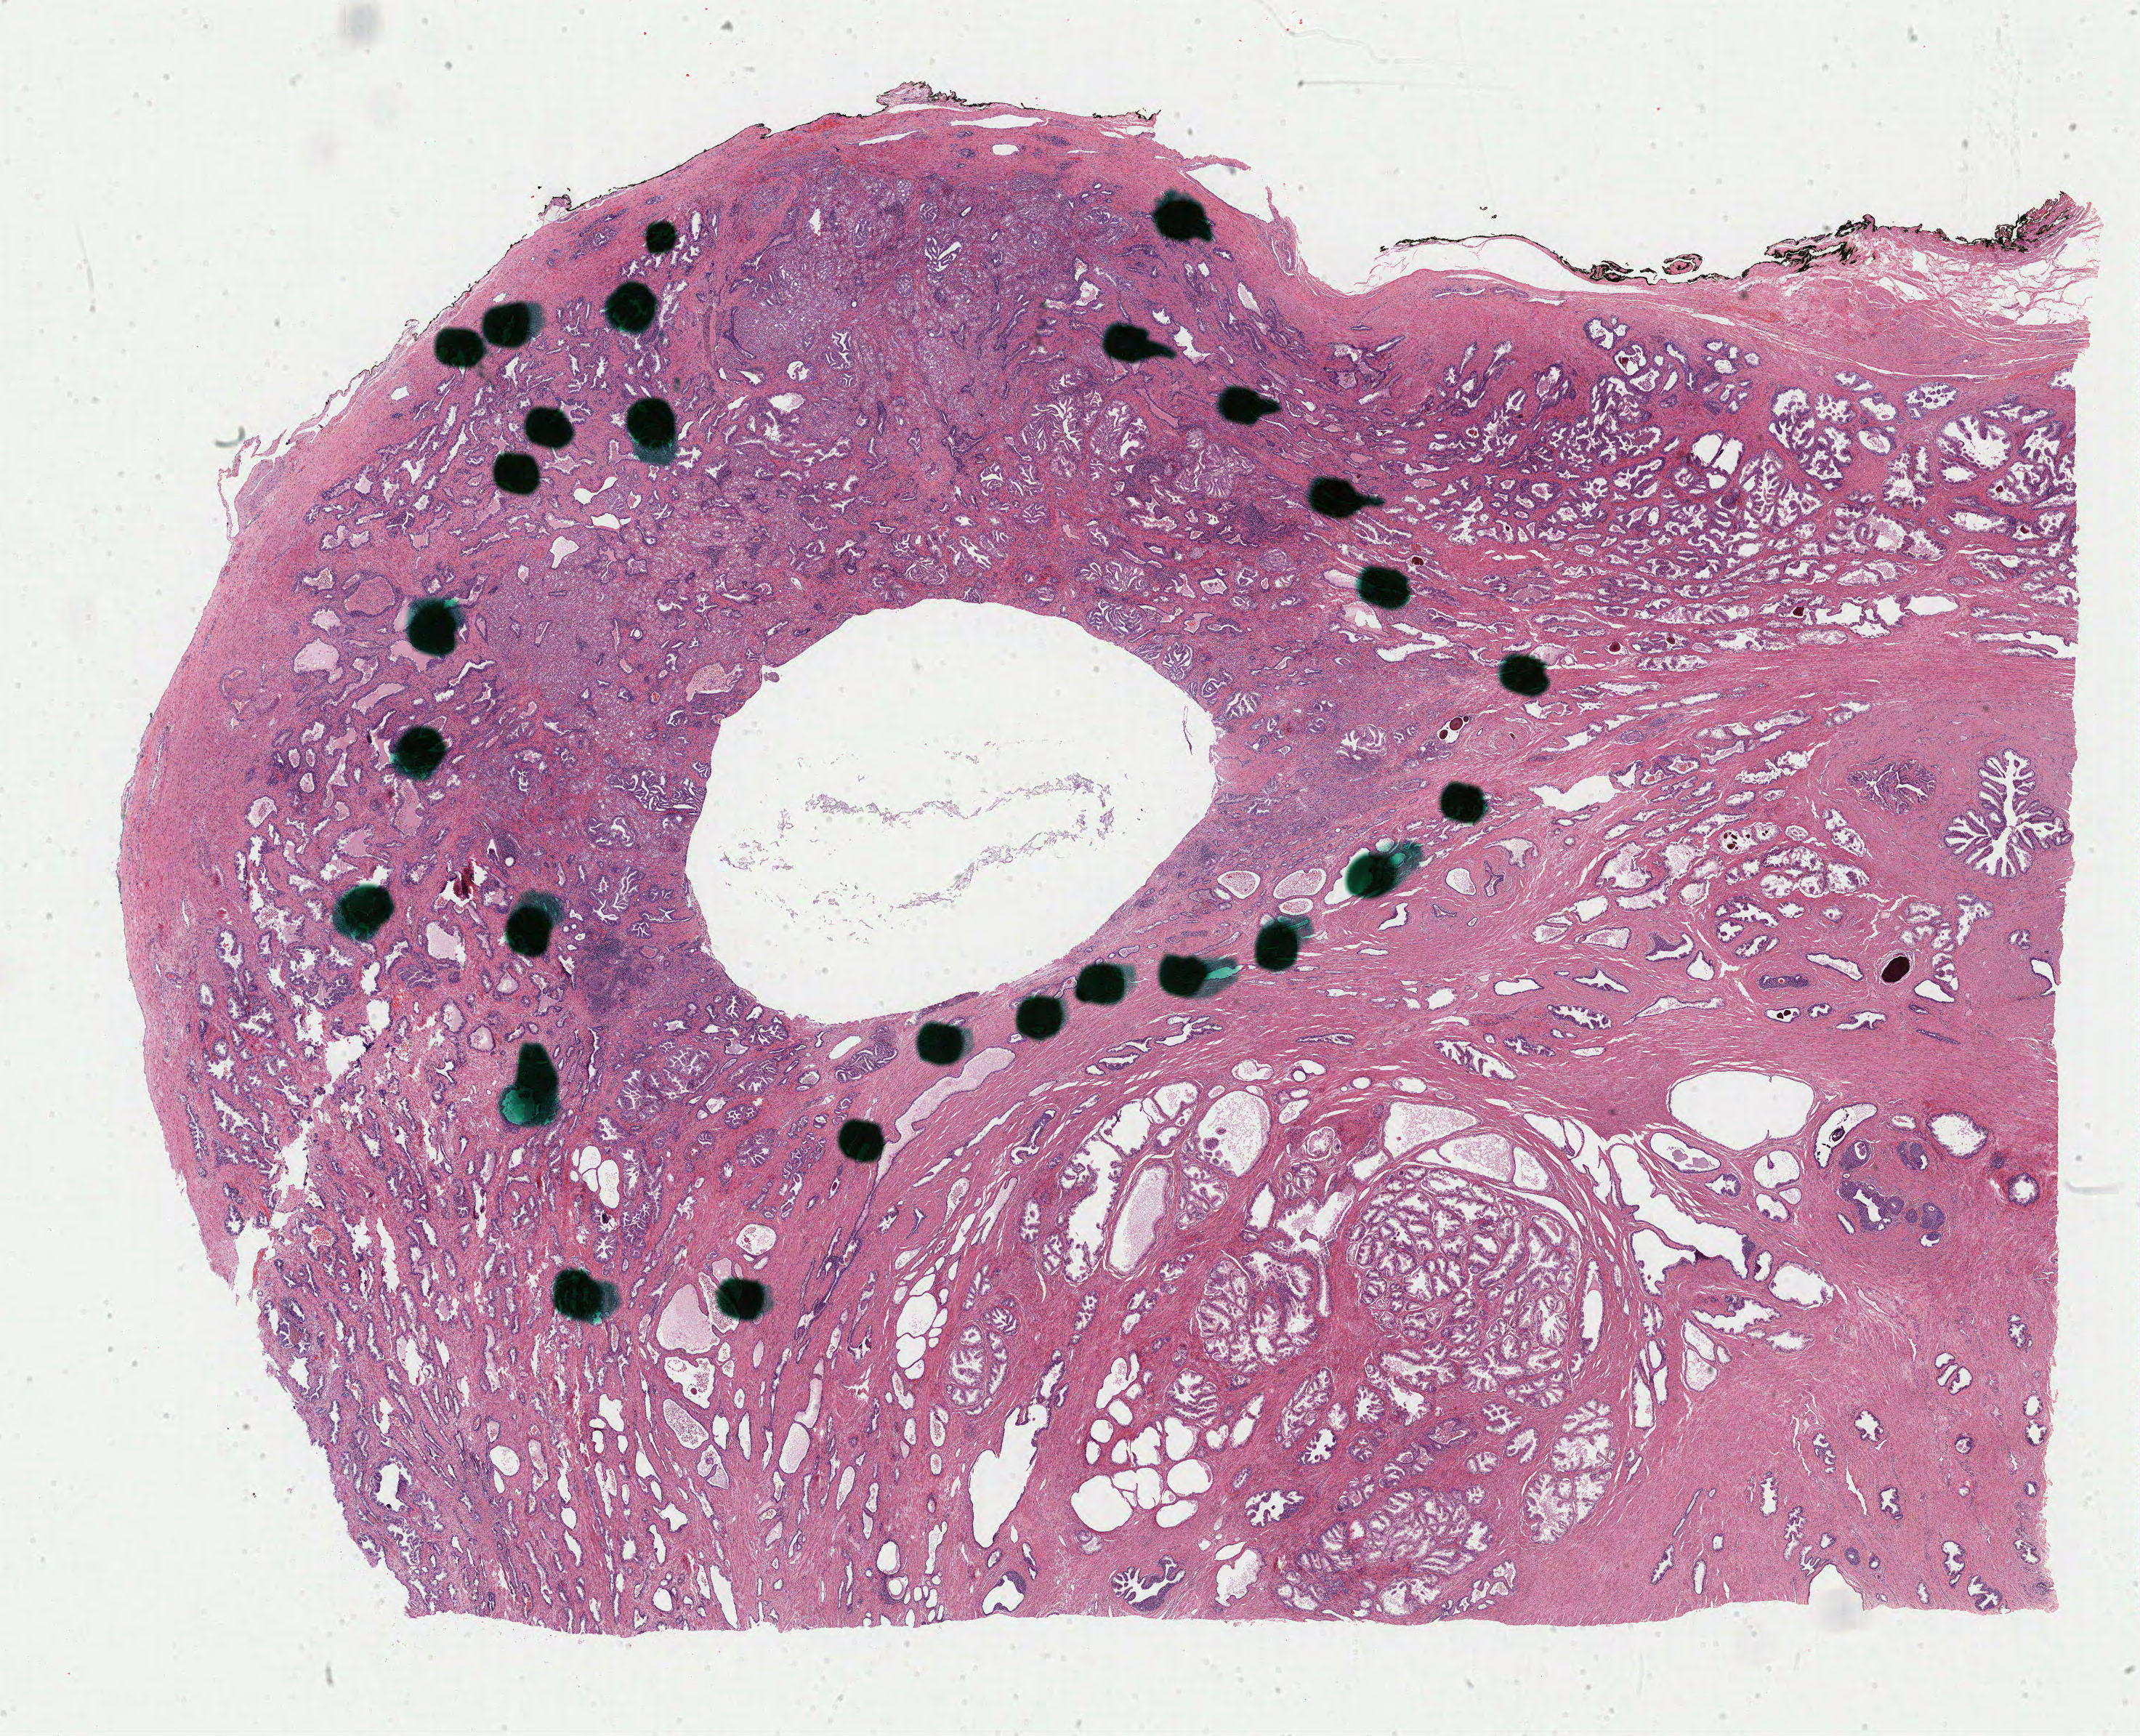
Digitized H&E tissue section (whole slide) — low-resolution overview of the scanned area, about 23.4 x 19.0 mm. Formalin-fixed paraffin-embedded (FFPE) diagnostic section. Primary tumour sample from the prostate. Patient: male, age at initial diagnosis 55 years. Gleason score: 7 (4+3).
* pathologic diagnosis: Adenocarcinoma, NOS (prostate gland)